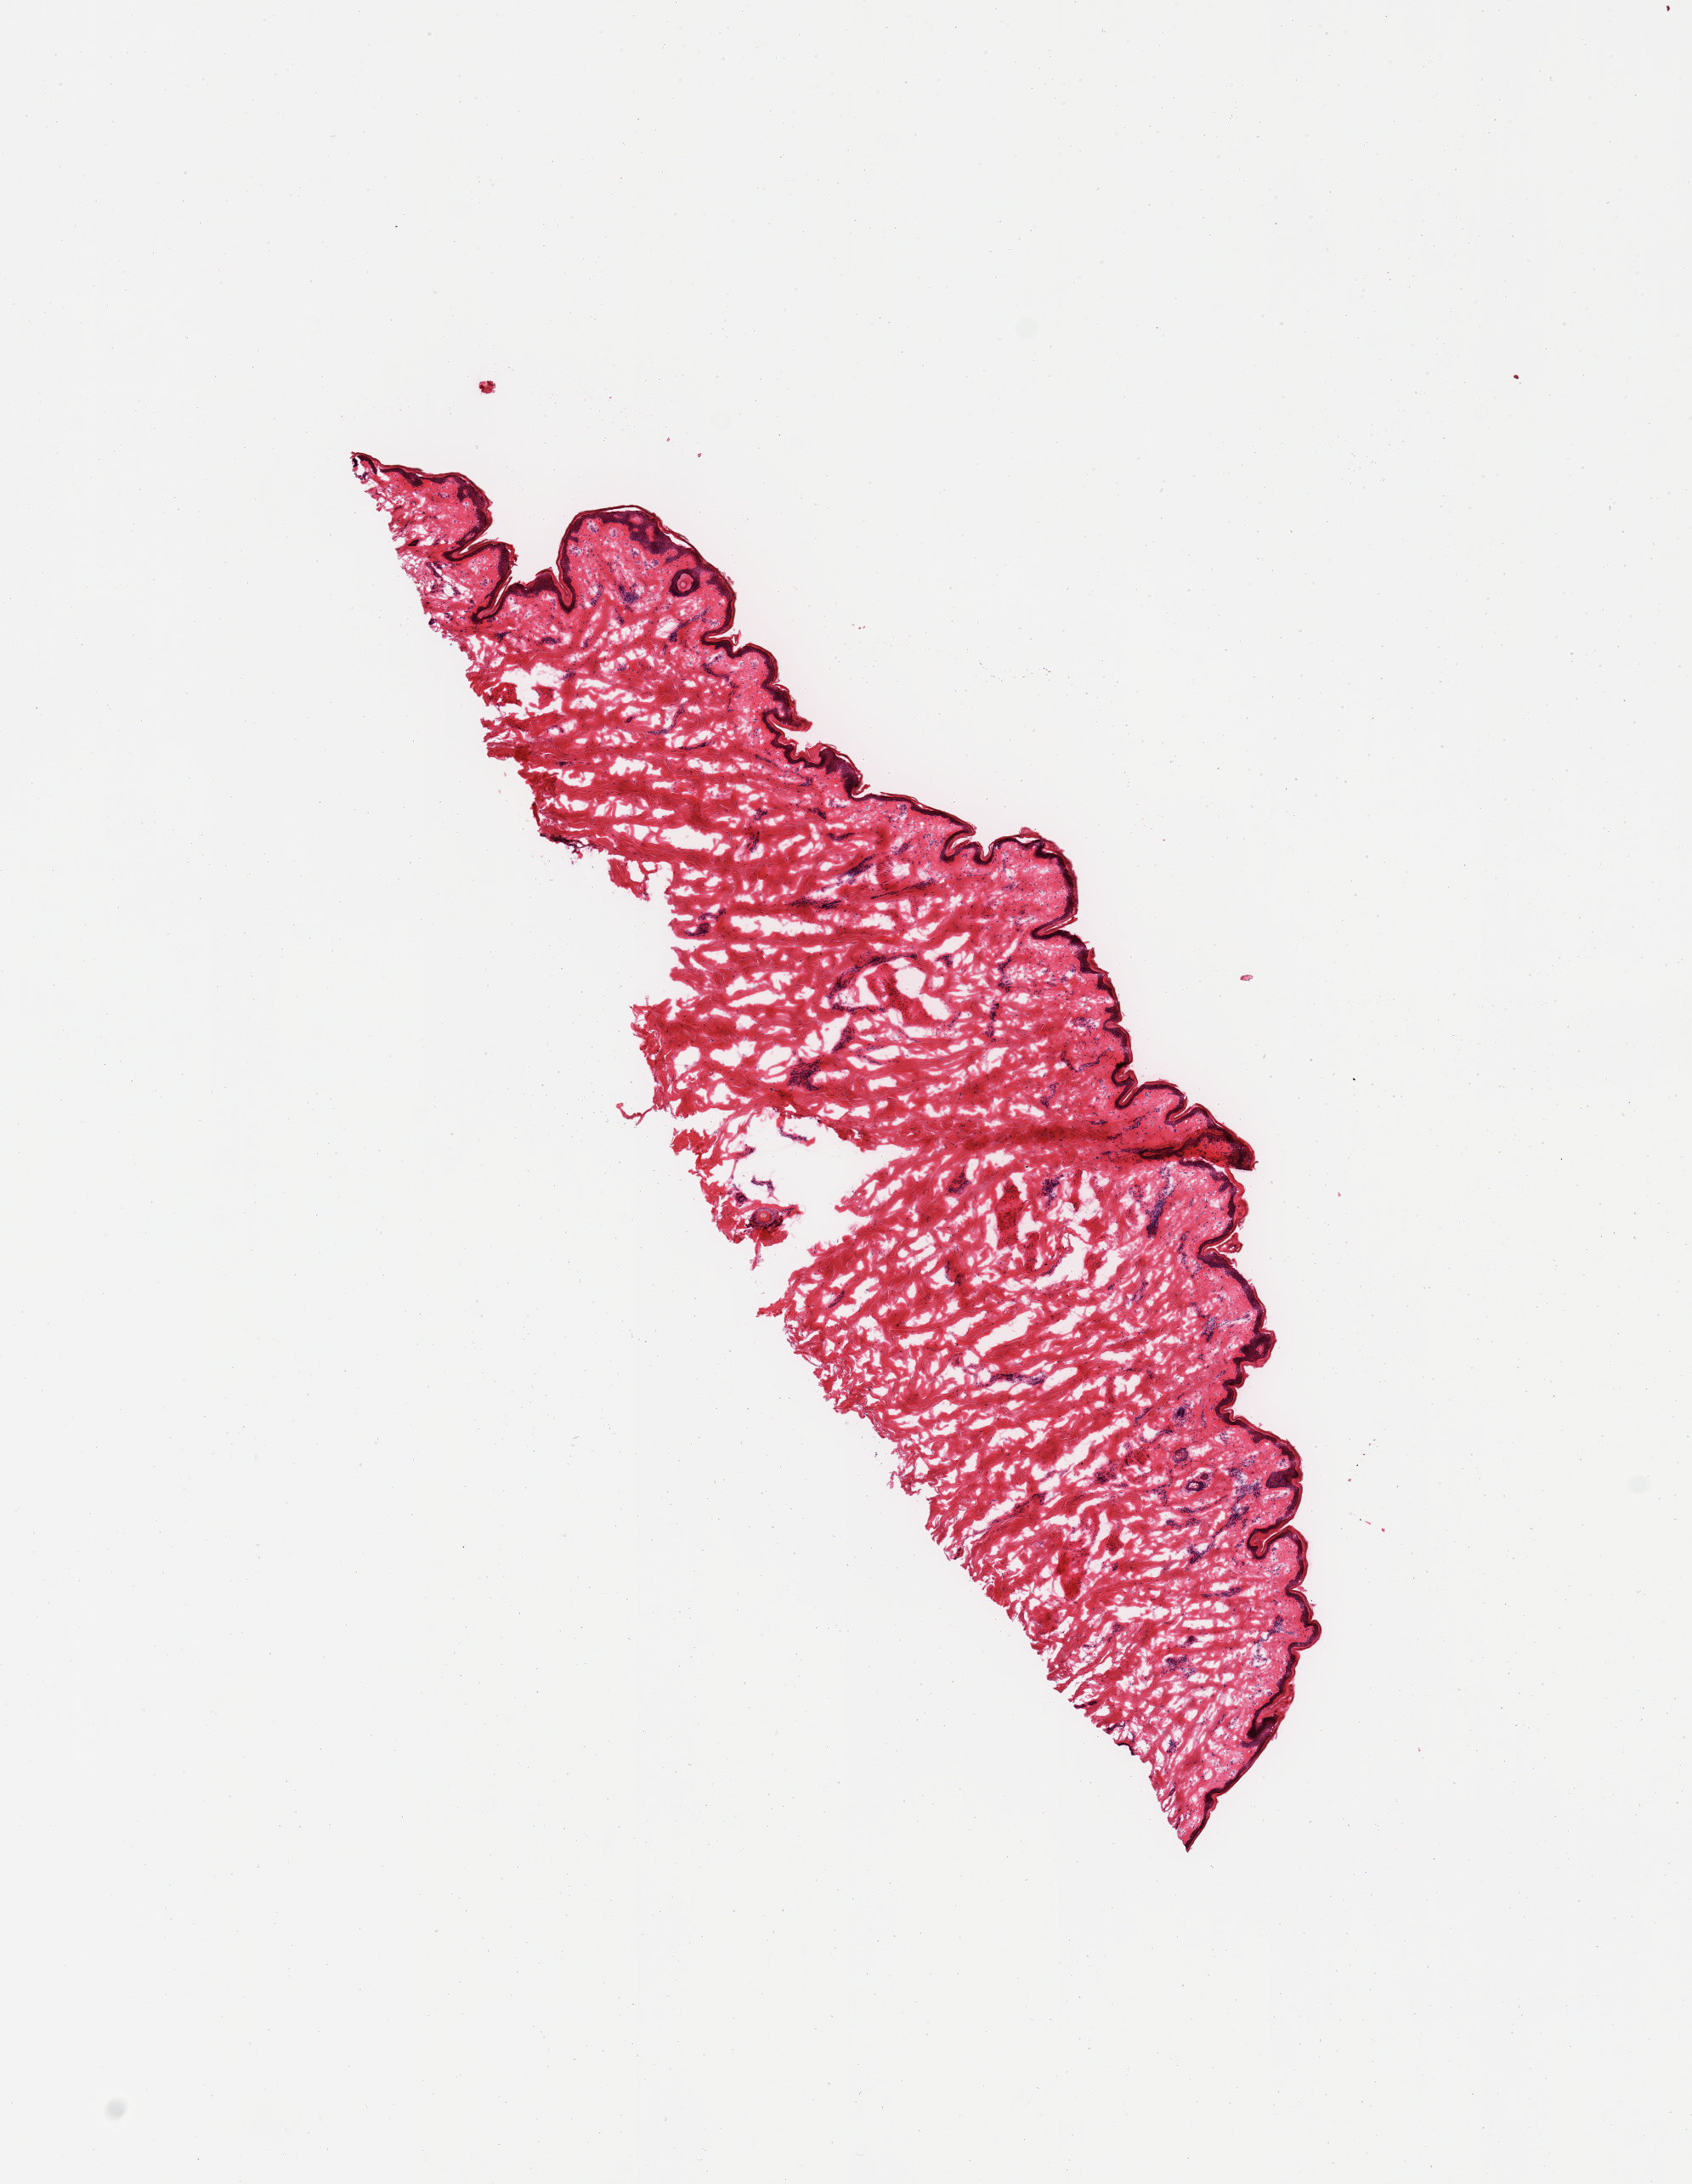
Whole-slide image, H&E stain, brightfield — low-resolution overview of the scanned area, about 7.9 x 10.2 mm. Donor sex: male.
Specimen: frozen section (dry ice); target tissue: skin of lower leg; donor tissue sample.